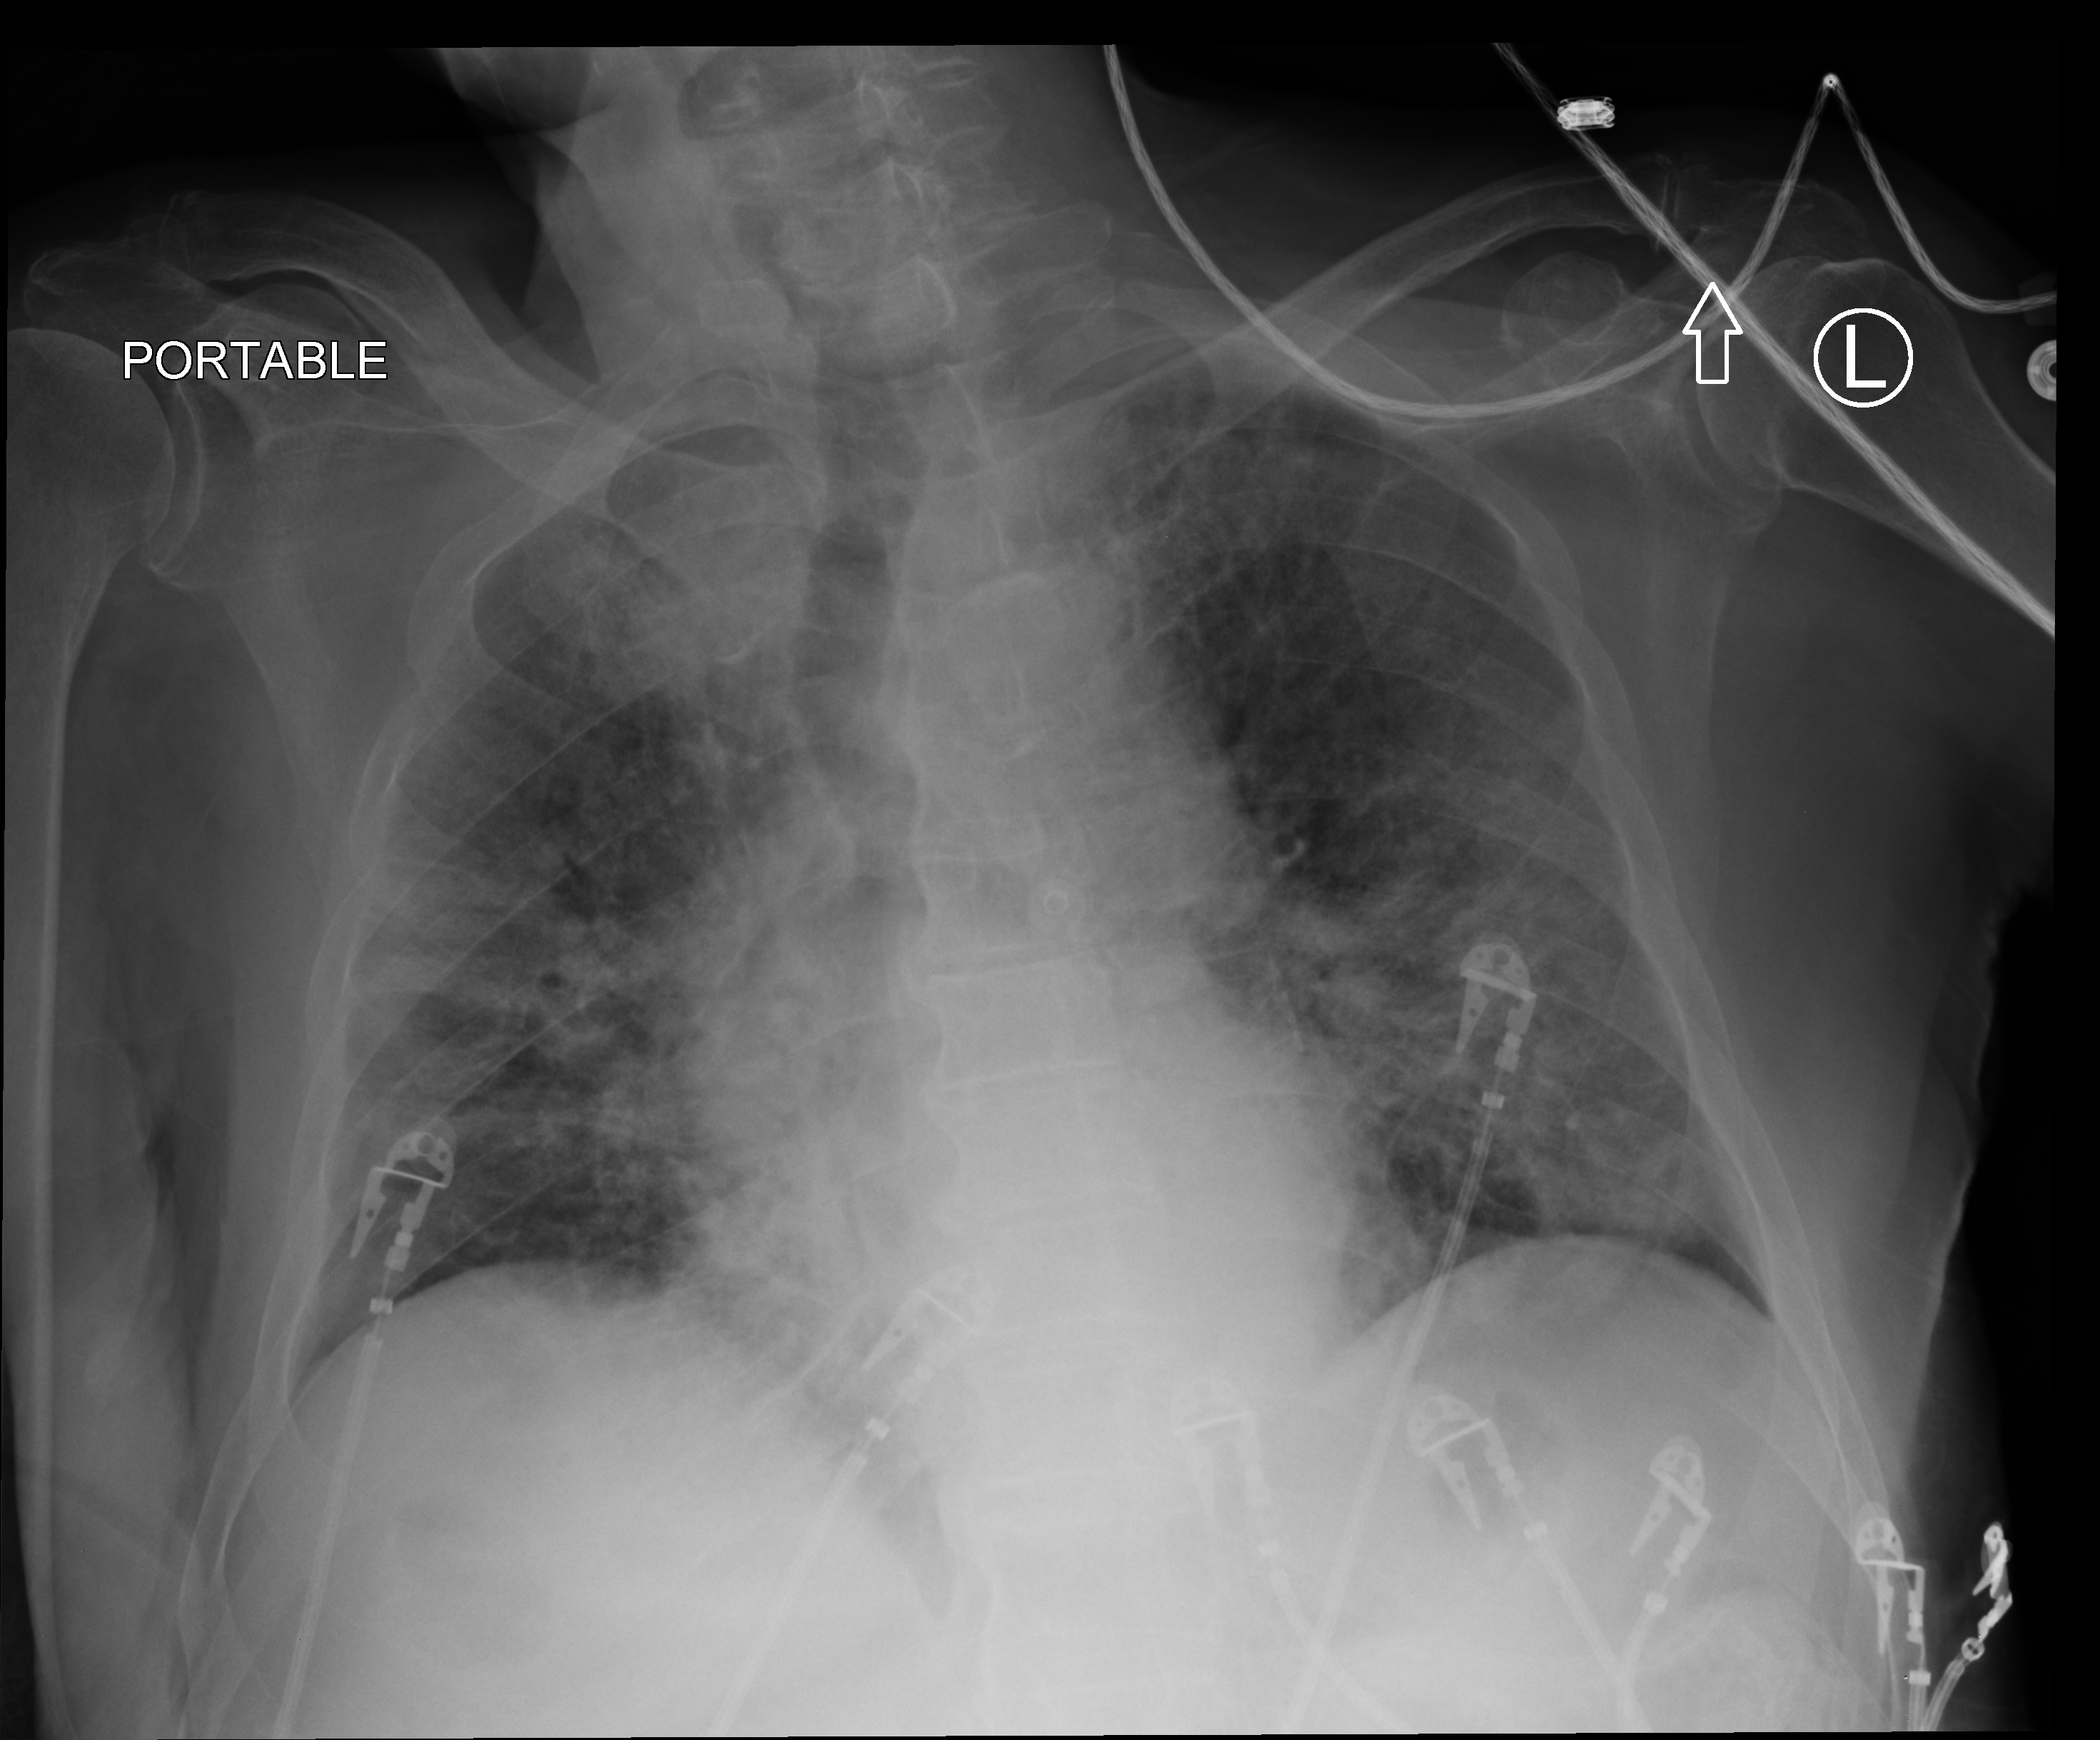
Bedside chest radiograph (computed radiography). Patient hospitalised with COVID-19; male, aged 75–90 years.
Admission-level facts for this patient (not findings on this image; timing relative to this image not recorded):
- length of hospital stay: 17 days